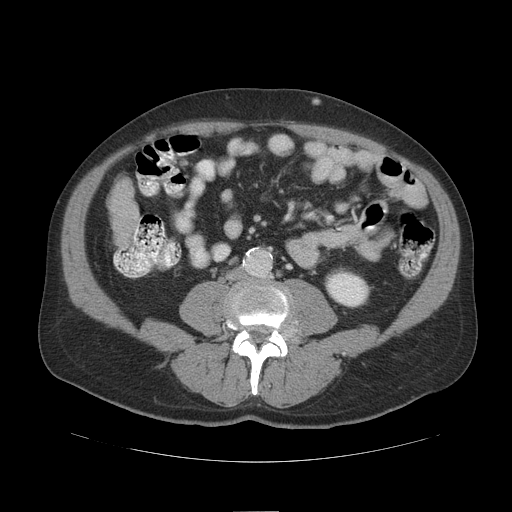
Contrast-enhanced abdominal CT (liver protocol), one axial slice; reconstruction kernel STANDARD; soft-tissue window (W 400 / L 40 HU); 512 × 512 image matrix, field of view 420 × 420 mm. From the clinical record (not read from this slice): diagnosis: hepatocellular carcinoma (patient treated with transarterial chemoembolisation; whether this scan precedes or follows treatment is not stated here); TNM stage (as recorded): Stage-IIIB; Child-Pugh class: A.
Outlined on this slice (semi-automatic segmentation, software-assisted and operator-edited):
- liver parenchyma outside the tumour (the mass and vessels are separate outlines, so this box may not span the whole liver): bounding box <110,178,140,248> (left, top, right, bottom; pixels)
- liver vessels: <134,230,138,240>